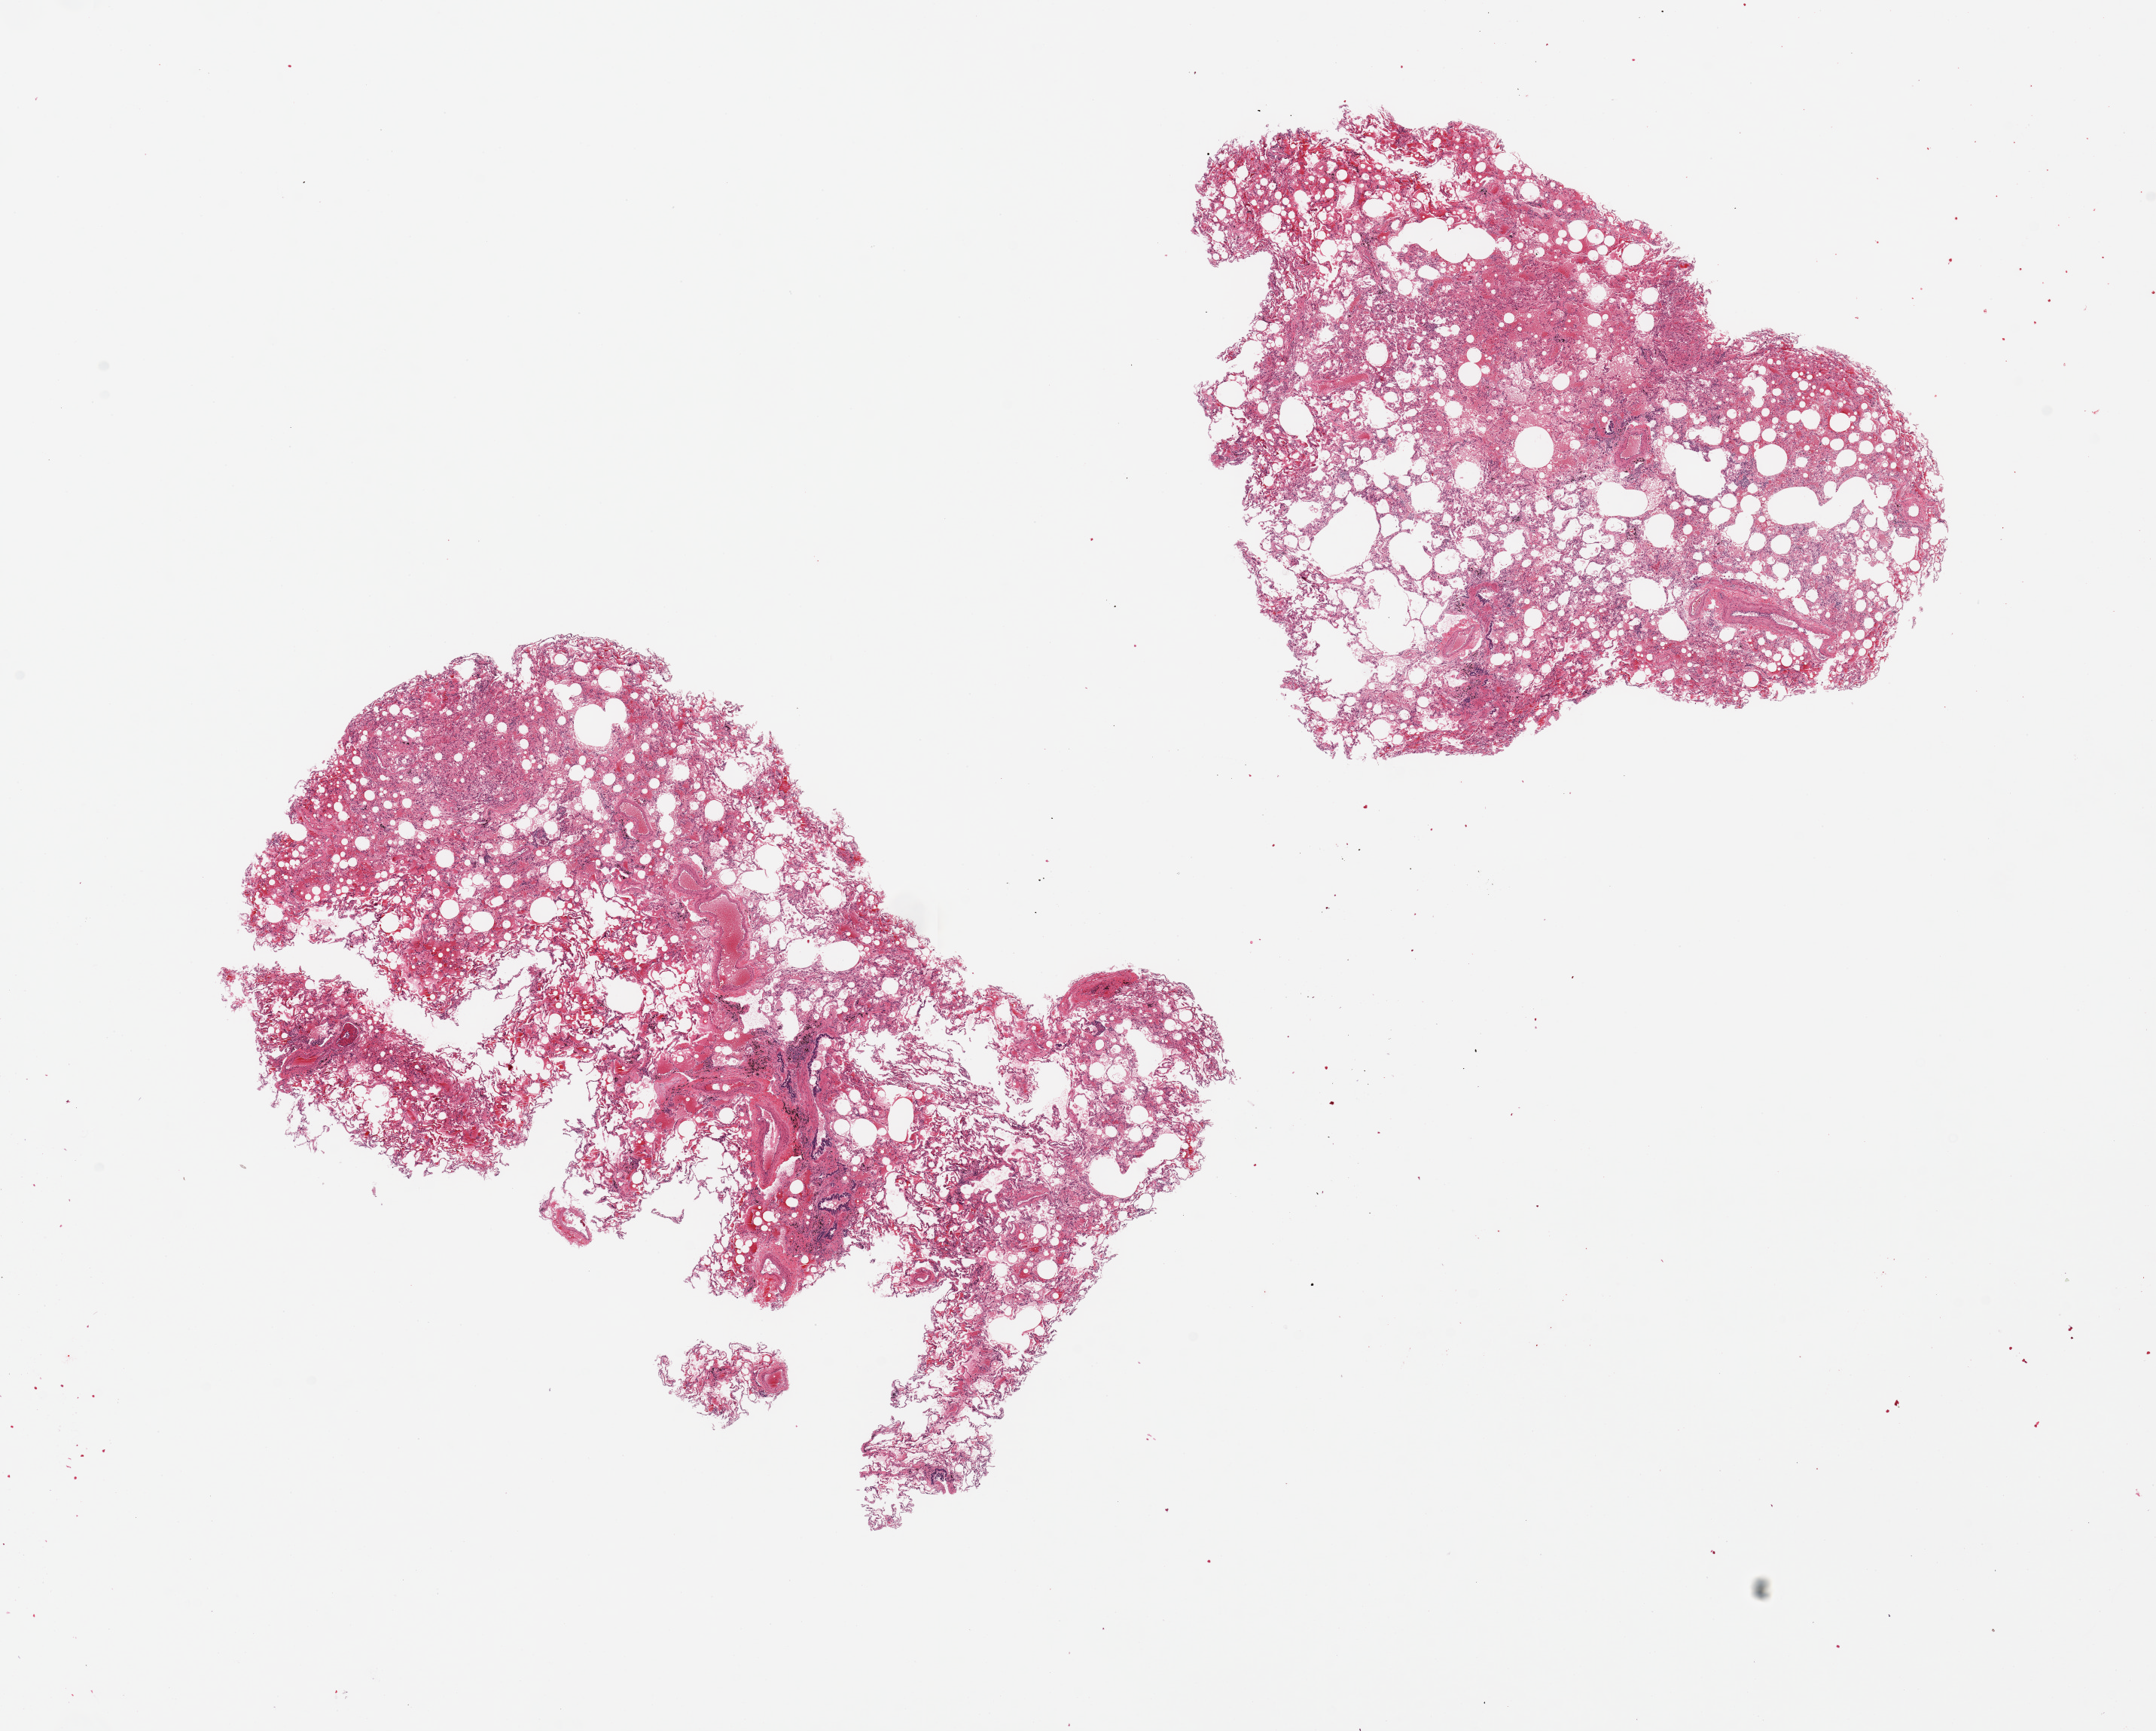
Whole-slide image, hematoxylin and eosin (H&E) stain — whole scanned area (about 22.6 x 18.2 mm) shown as a low-resolution overview; PAXgene-fixed, paraffin-embedded tissue; sampled site (target tissue): lung; tissue donor sample.
- review note (as recorded): 2 pieces. Patchy alveolar hemorrhage, emphysema, fibrosis; carbon pigment